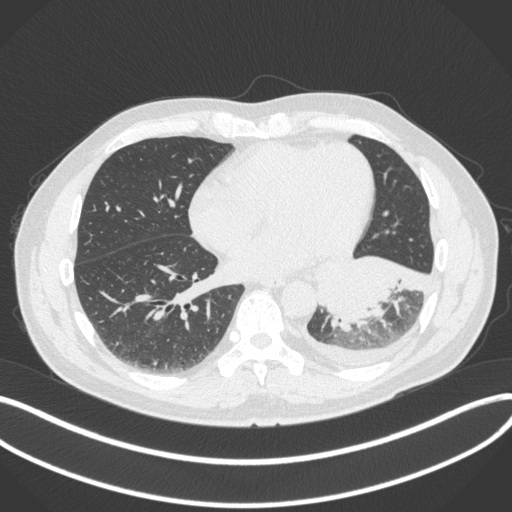
Chest CT, one axial slice. Slice 134 of 350 in the series (ordered by position). Reconstruction kernel B31f. Lung window (W 1500 / L -600 HU). 1 mm slice thickness. 512 × 512 image matrix, field of view 400 × 400 mm. Patient: male, 58 years. From the clinical record (not read from this slice): clinical TNM (as recorded): T3 N1 M1b.
Structures marked on this image (rectangle marked by the reading radiologist):
- lung tumour (recorded histology: small cell carcinoma): bounding box (x1, y1, x2, y2) in pixels: (313, 246, 432, 331)